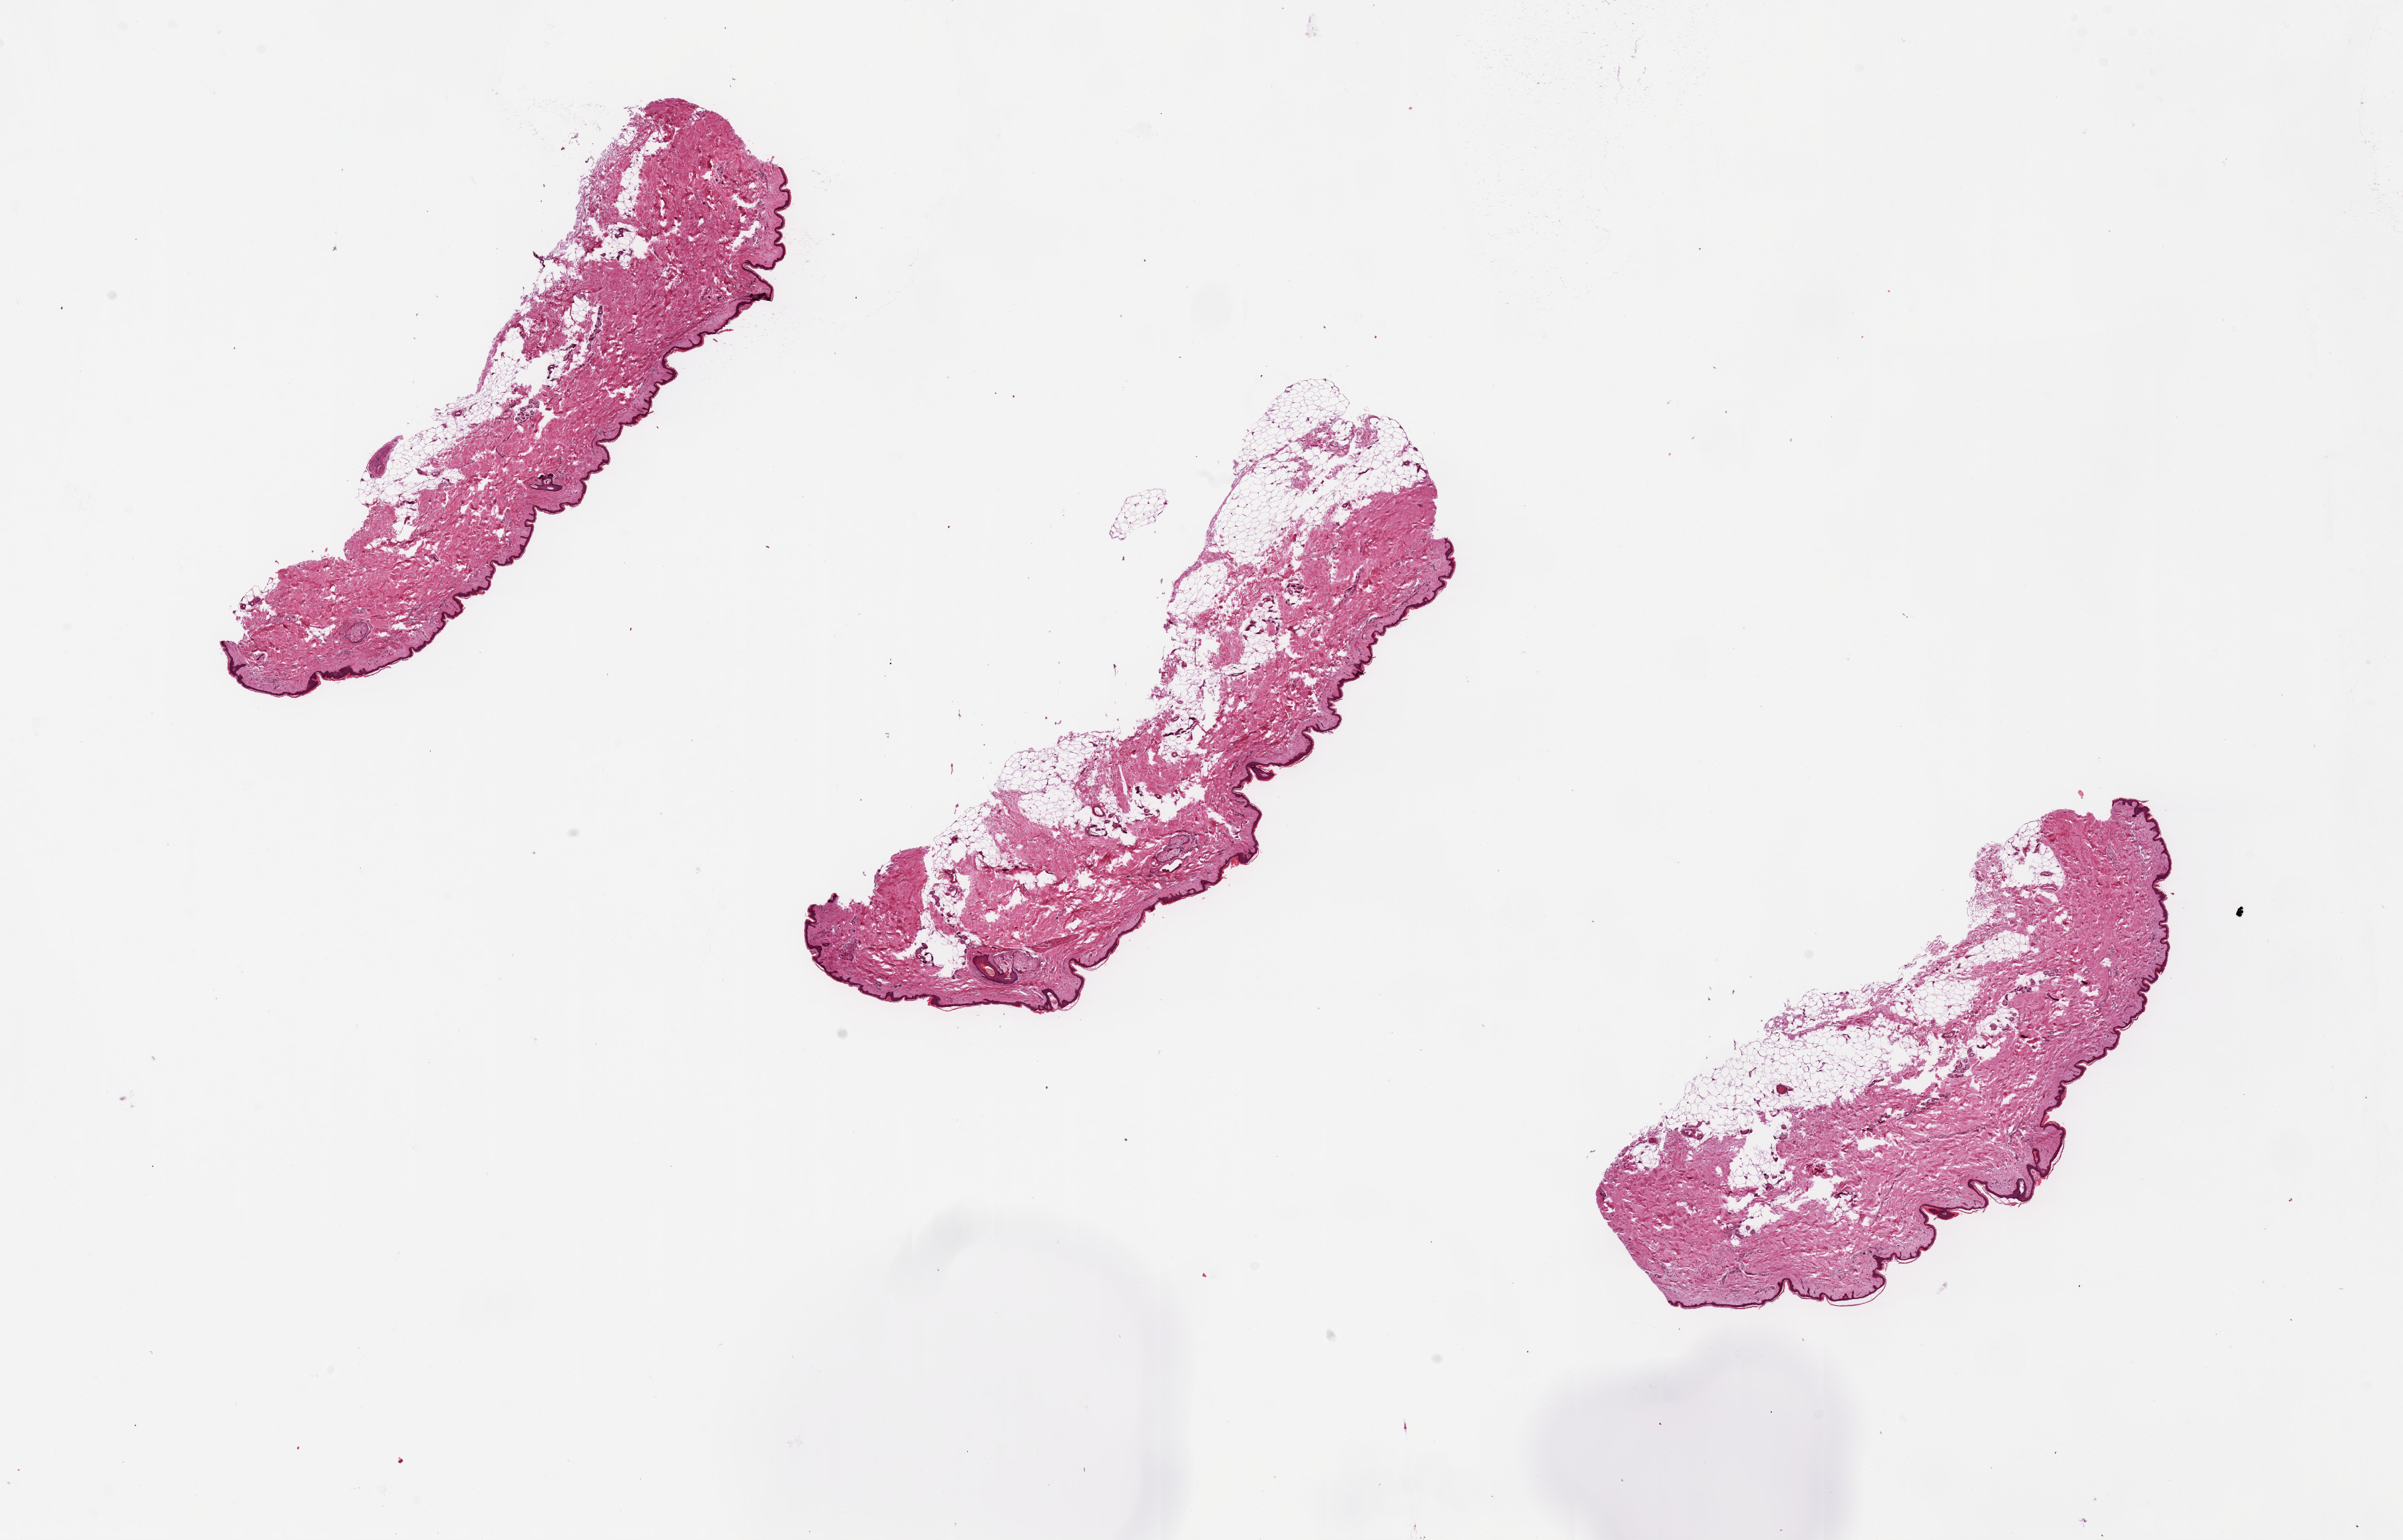
Digitized haematoxylin and eosin-stained section, shown as a low-resolution overview of the whole scanned area (about 28.5 x 18.3 mm, slide scanned at 20x). PAXgene-fixed, paraffin-embedded tissue. Sampled site (target tissue): skin of lower leg. Tissue donor sample. Male donor.
Pathologist's review note for this sample: 3 pieces.